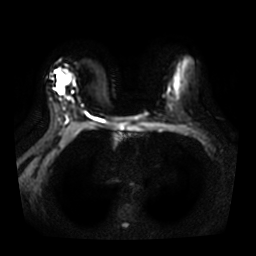
Breast MRI, one axial slice; slice 20 of 31 in the series (ordered by position); diffusion-weighted series; image 2 of 4 stored at this slice position (different b-values; order by instance number); 3 T; 5 mm slice thickness; 256 × 256 image matrix, field of view 350 × 350 mm. Female patient.
Annotated regions visible in this slice (outlined manually by an expert reader):
- tumour on diffusion-weighted imaging: bounding box <57,80,64,87> (left, top, right, bottom; pixels)